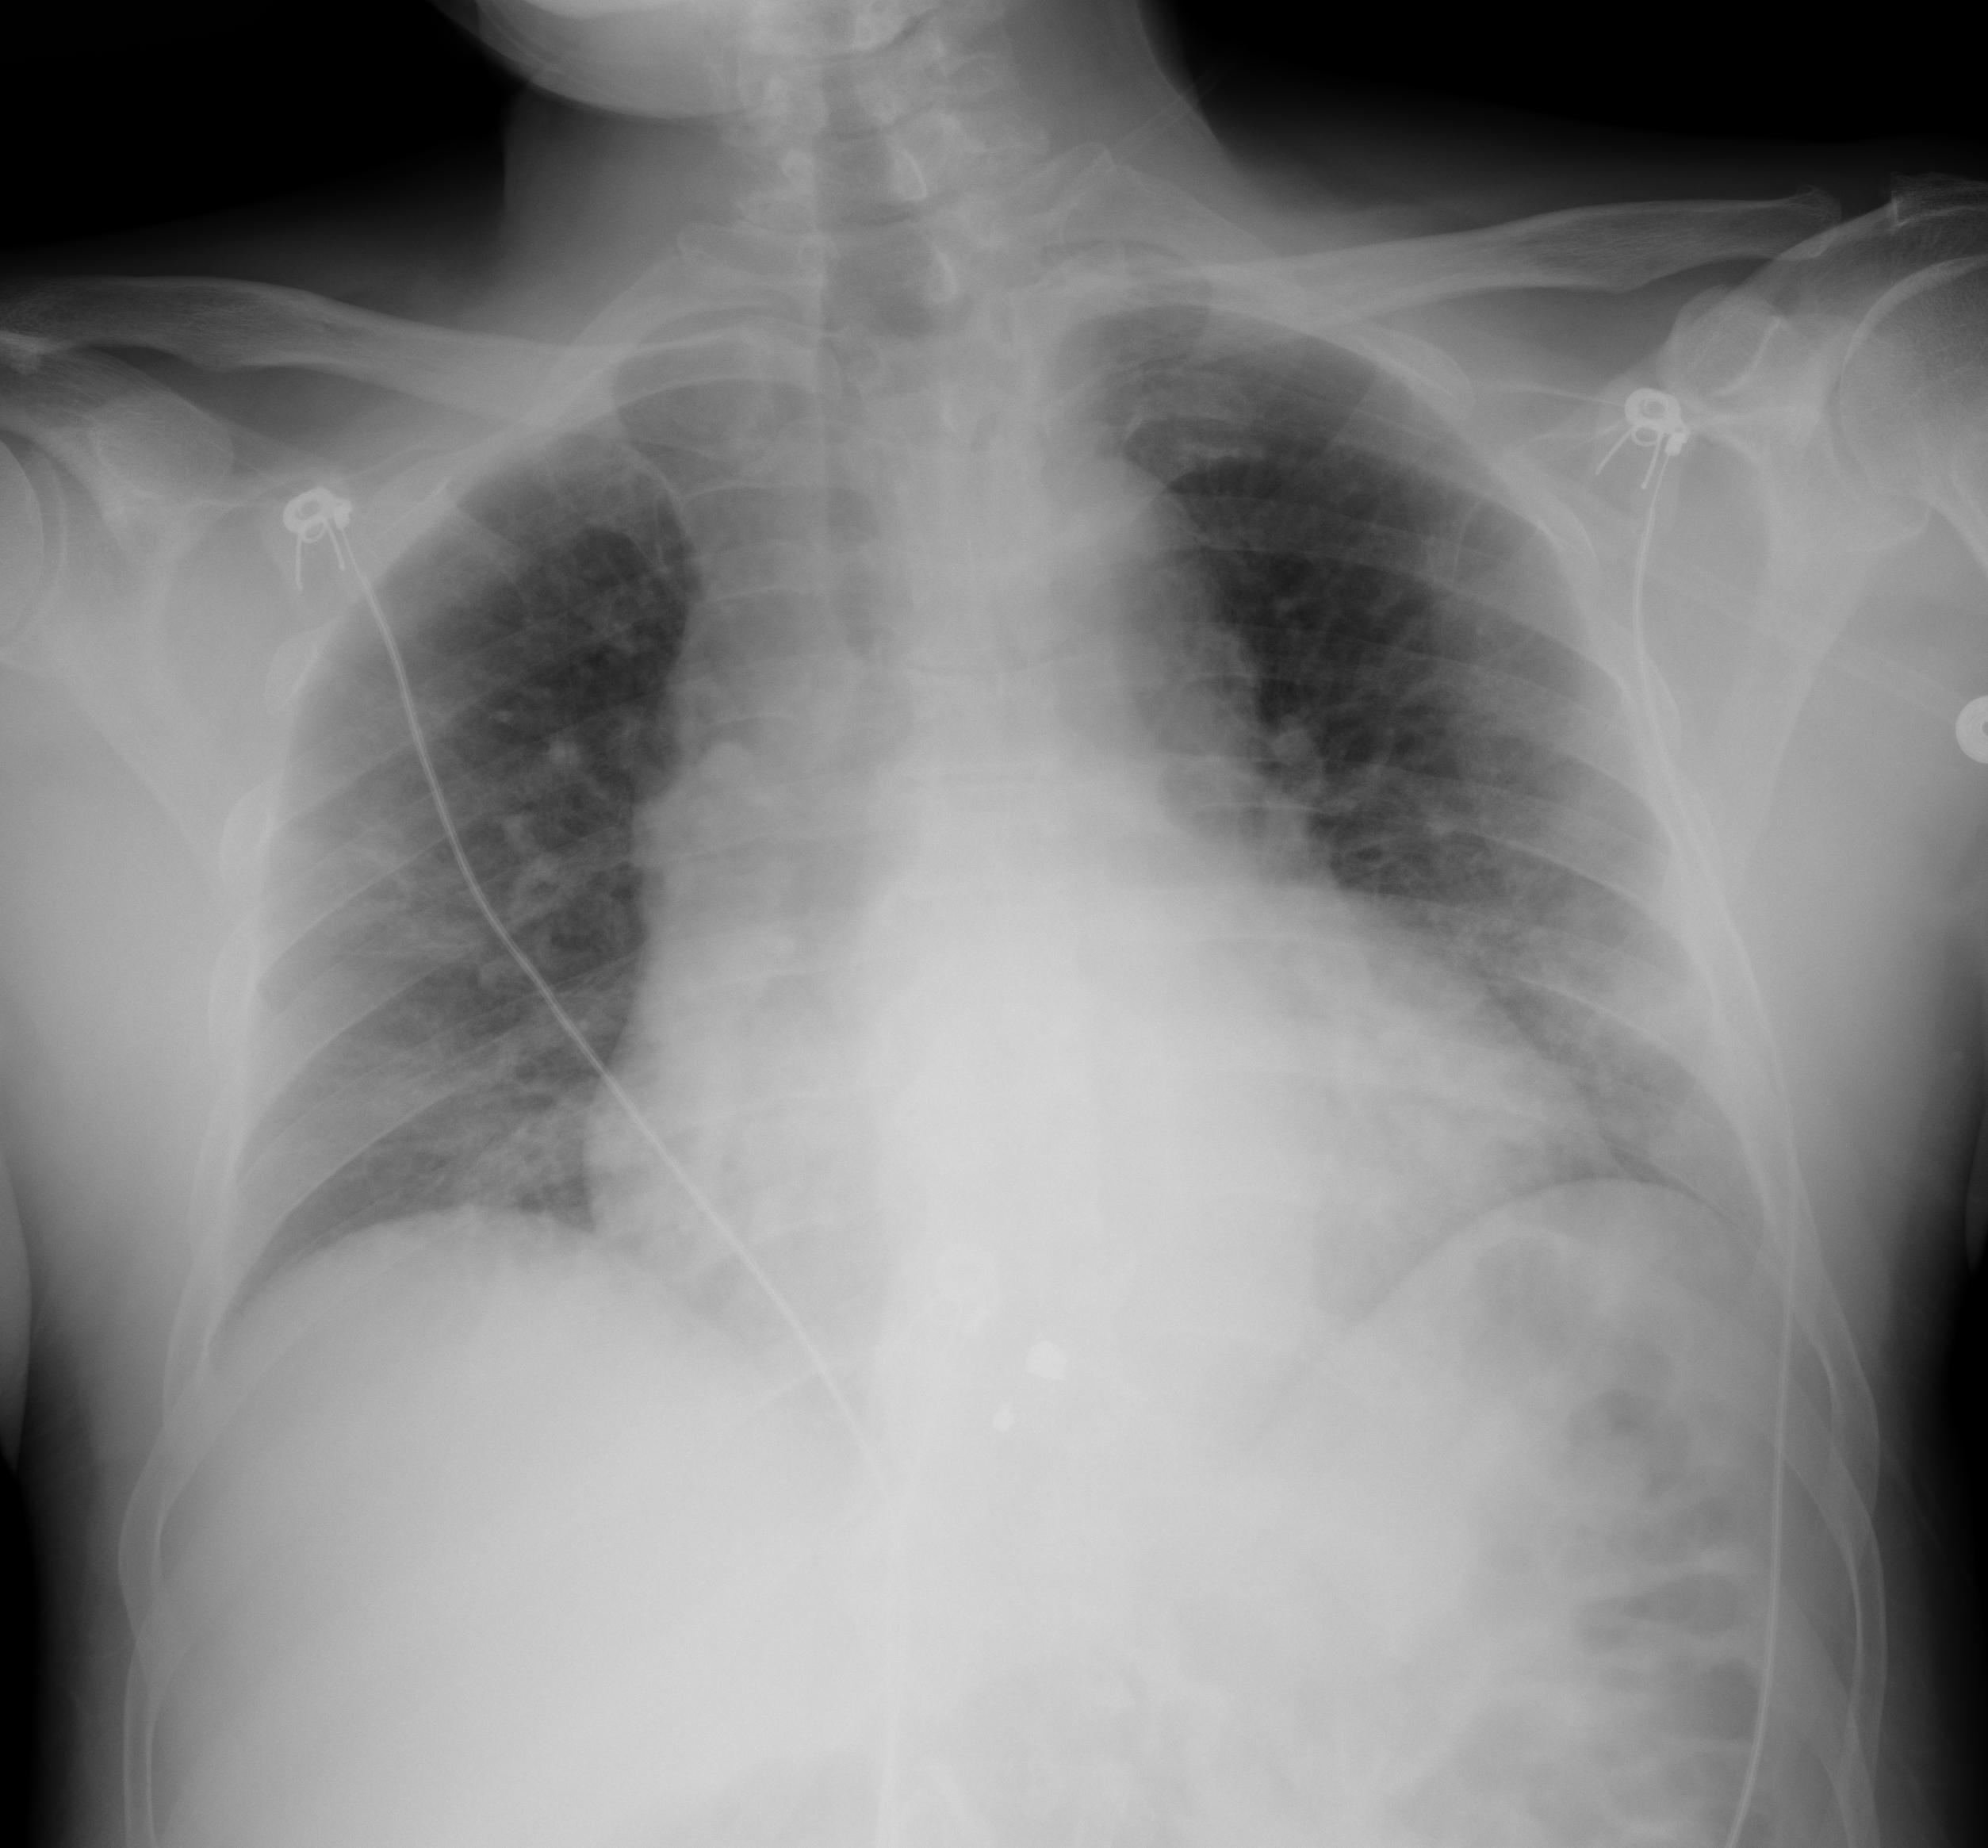
Portable chest radiograph, AP projection. Male patient, age 57 years; imaged 0 days after the COVID-19 diagnosis.
Radiologist's key findings for this exam: Bibasilar opacities.